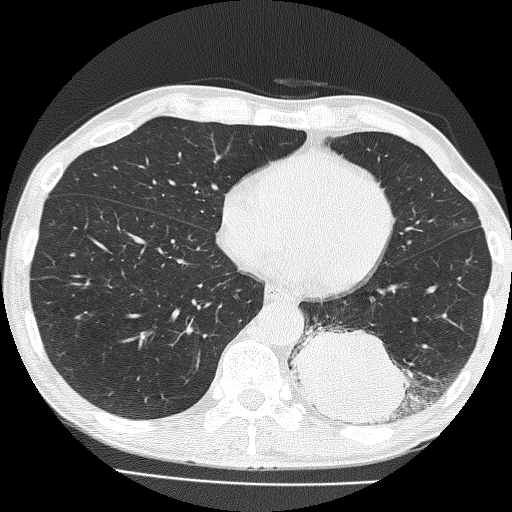
Low-dose screening chest CT, axial slice. First (baseline) screen. Lung window (W 1500 / L -600 HU). 2 mm slice thickness. Slice 101 of 160 in the series. 512 × 512 image matrix, field of view 324 × 324 mm. Male participant, aged 58 years at enrolment. Current smoker at enrolment.
Expert-annotated lung lesion, bounding box <294,300,426,434> (left, top, right, bottom; pixels). The screening reader recorded 2 non-calcified nodules or masses ≥4 mm on this exam (left lower lobe, left upper lobe); which of them this box marks is not recorded. Lung cancer was diagnosed 39 days after this screen: non-small cell carcinoma, left lower lobe, poorly differentiated (G3), stage IV (AJCC 6th edition), 74 mm at pathology.